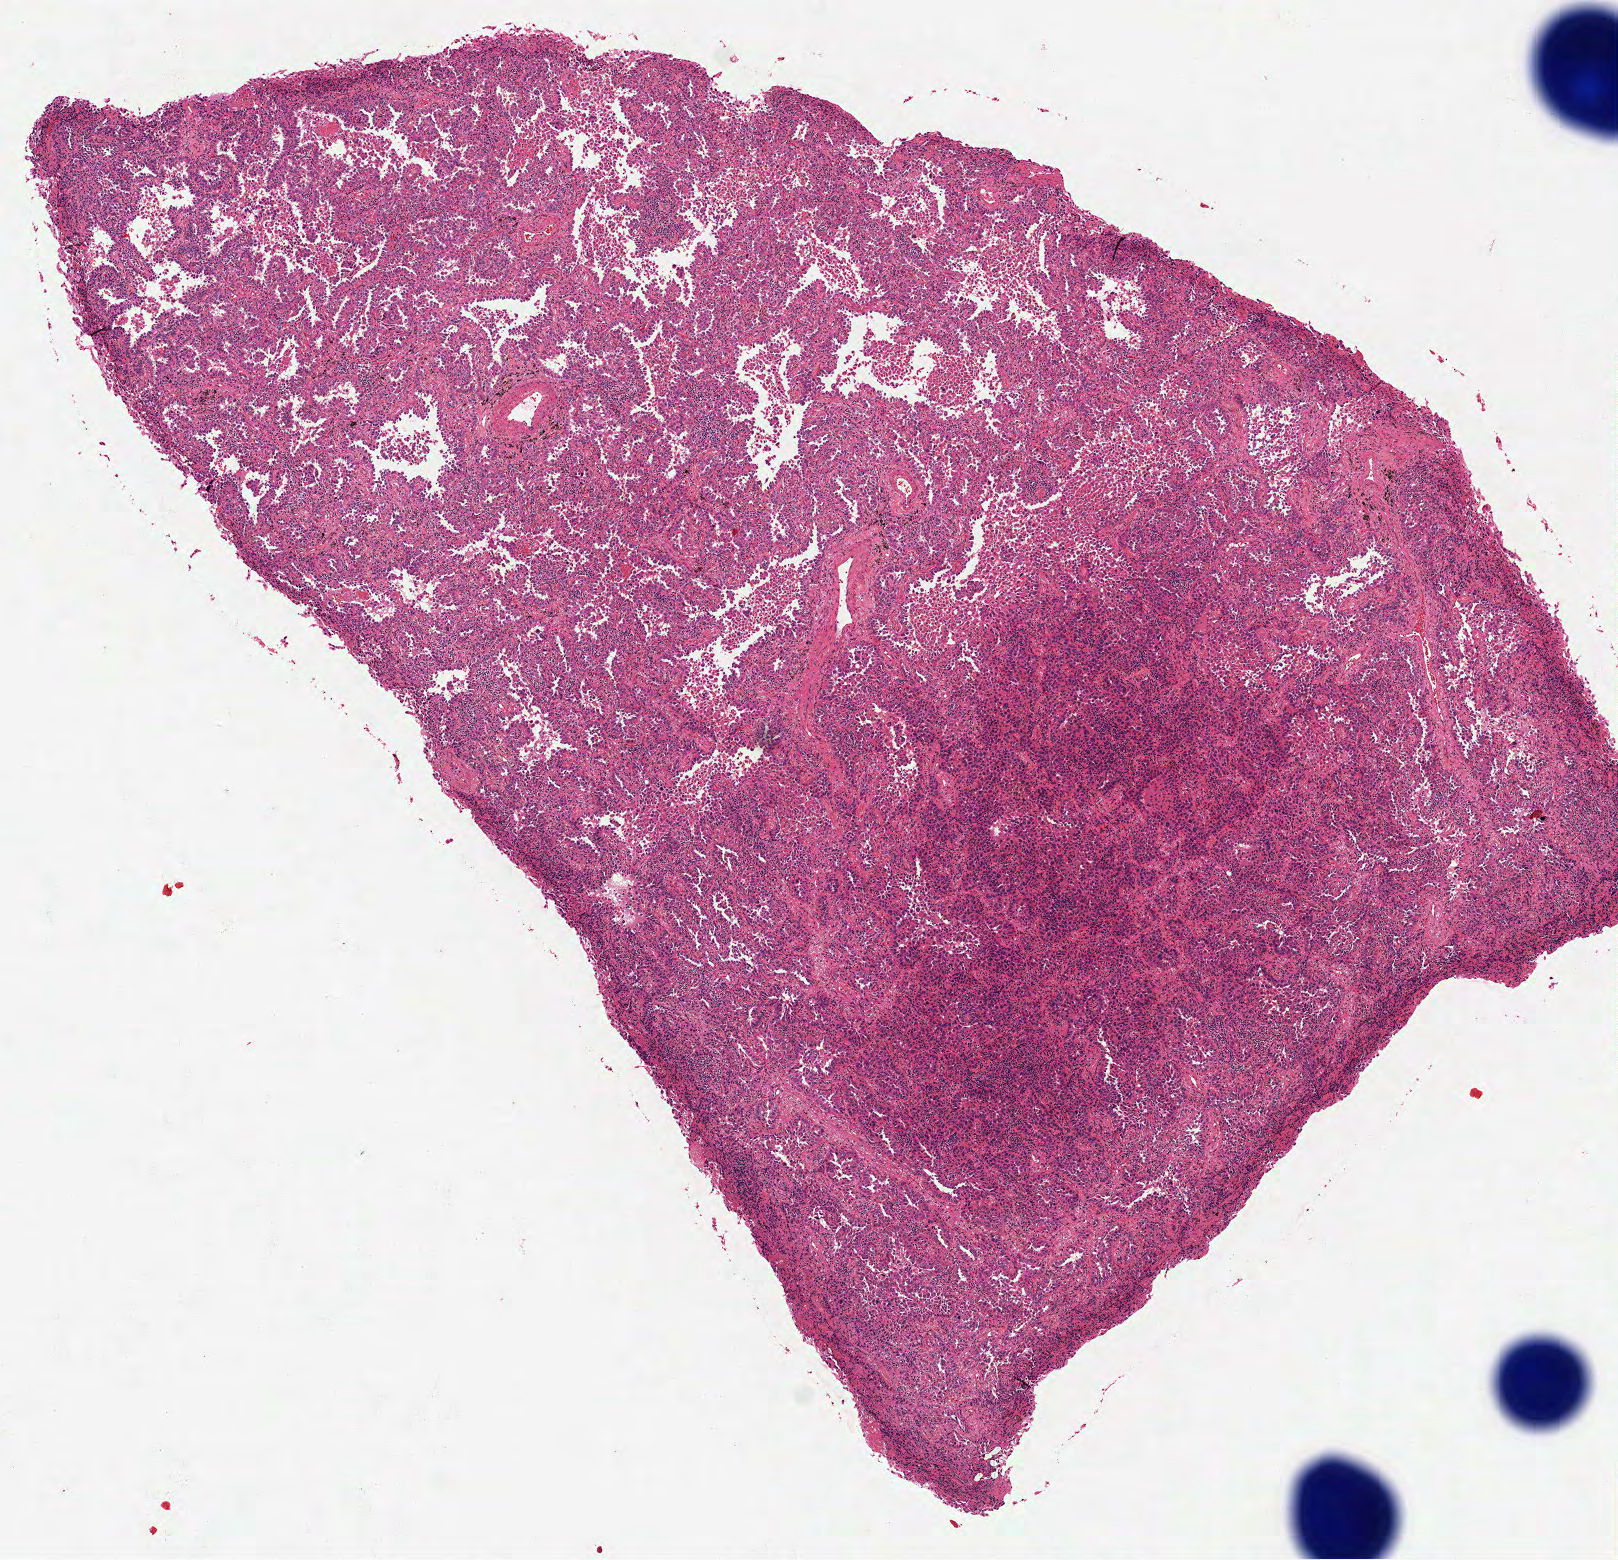
Whole-slide histology image, H&E, shown as a low-resolution overview of the whole scanned area (about 6.5 x 6.3 mm); frozen section; sample: primary tumour, lung. Female, age 75 years at initial diagnosis. Pathologist review of this section (percent, as recorded): tumour cells 100%, tumour nuclei 70%, normal cells 0%, stromal cells 0%, necrosis 0%. Inflammatory infiltration, as recorded: lymphocyte infiltration 15%, monocyte infiltration 0%, neutrophil infiltration 0%.
- laterality: right
- histologic diagnosis: Adenocarcinoma with mixed subtypes (upper lobe, lung)
- AJCC pathologic stage: IIA (7th edition)